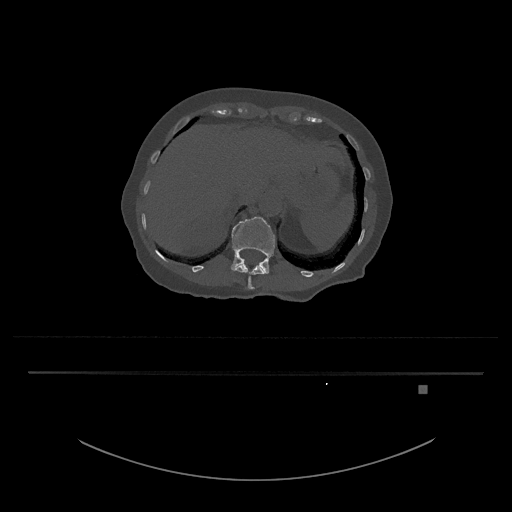
CT including the spine, one axial slice; reconstruction kernel Br40s/3; bone window (W 1800 / L 400 HU); 0.5 mm slice thickness; 512 × 512 image matrix, field of view 500 × 500 mm. Female patient, age 57 years. Case-level facts recorded for this patient, not image findings: primary cancer: cervical.
Outlined on this slice (semi-automatic segmentation, software-assisted and operator-edited):
- L1 vertebra: box from (x=231, y=217) to (x=275, y=274) px
- T12 vertebra: (x=235, y=262)–(x=265, y=289)